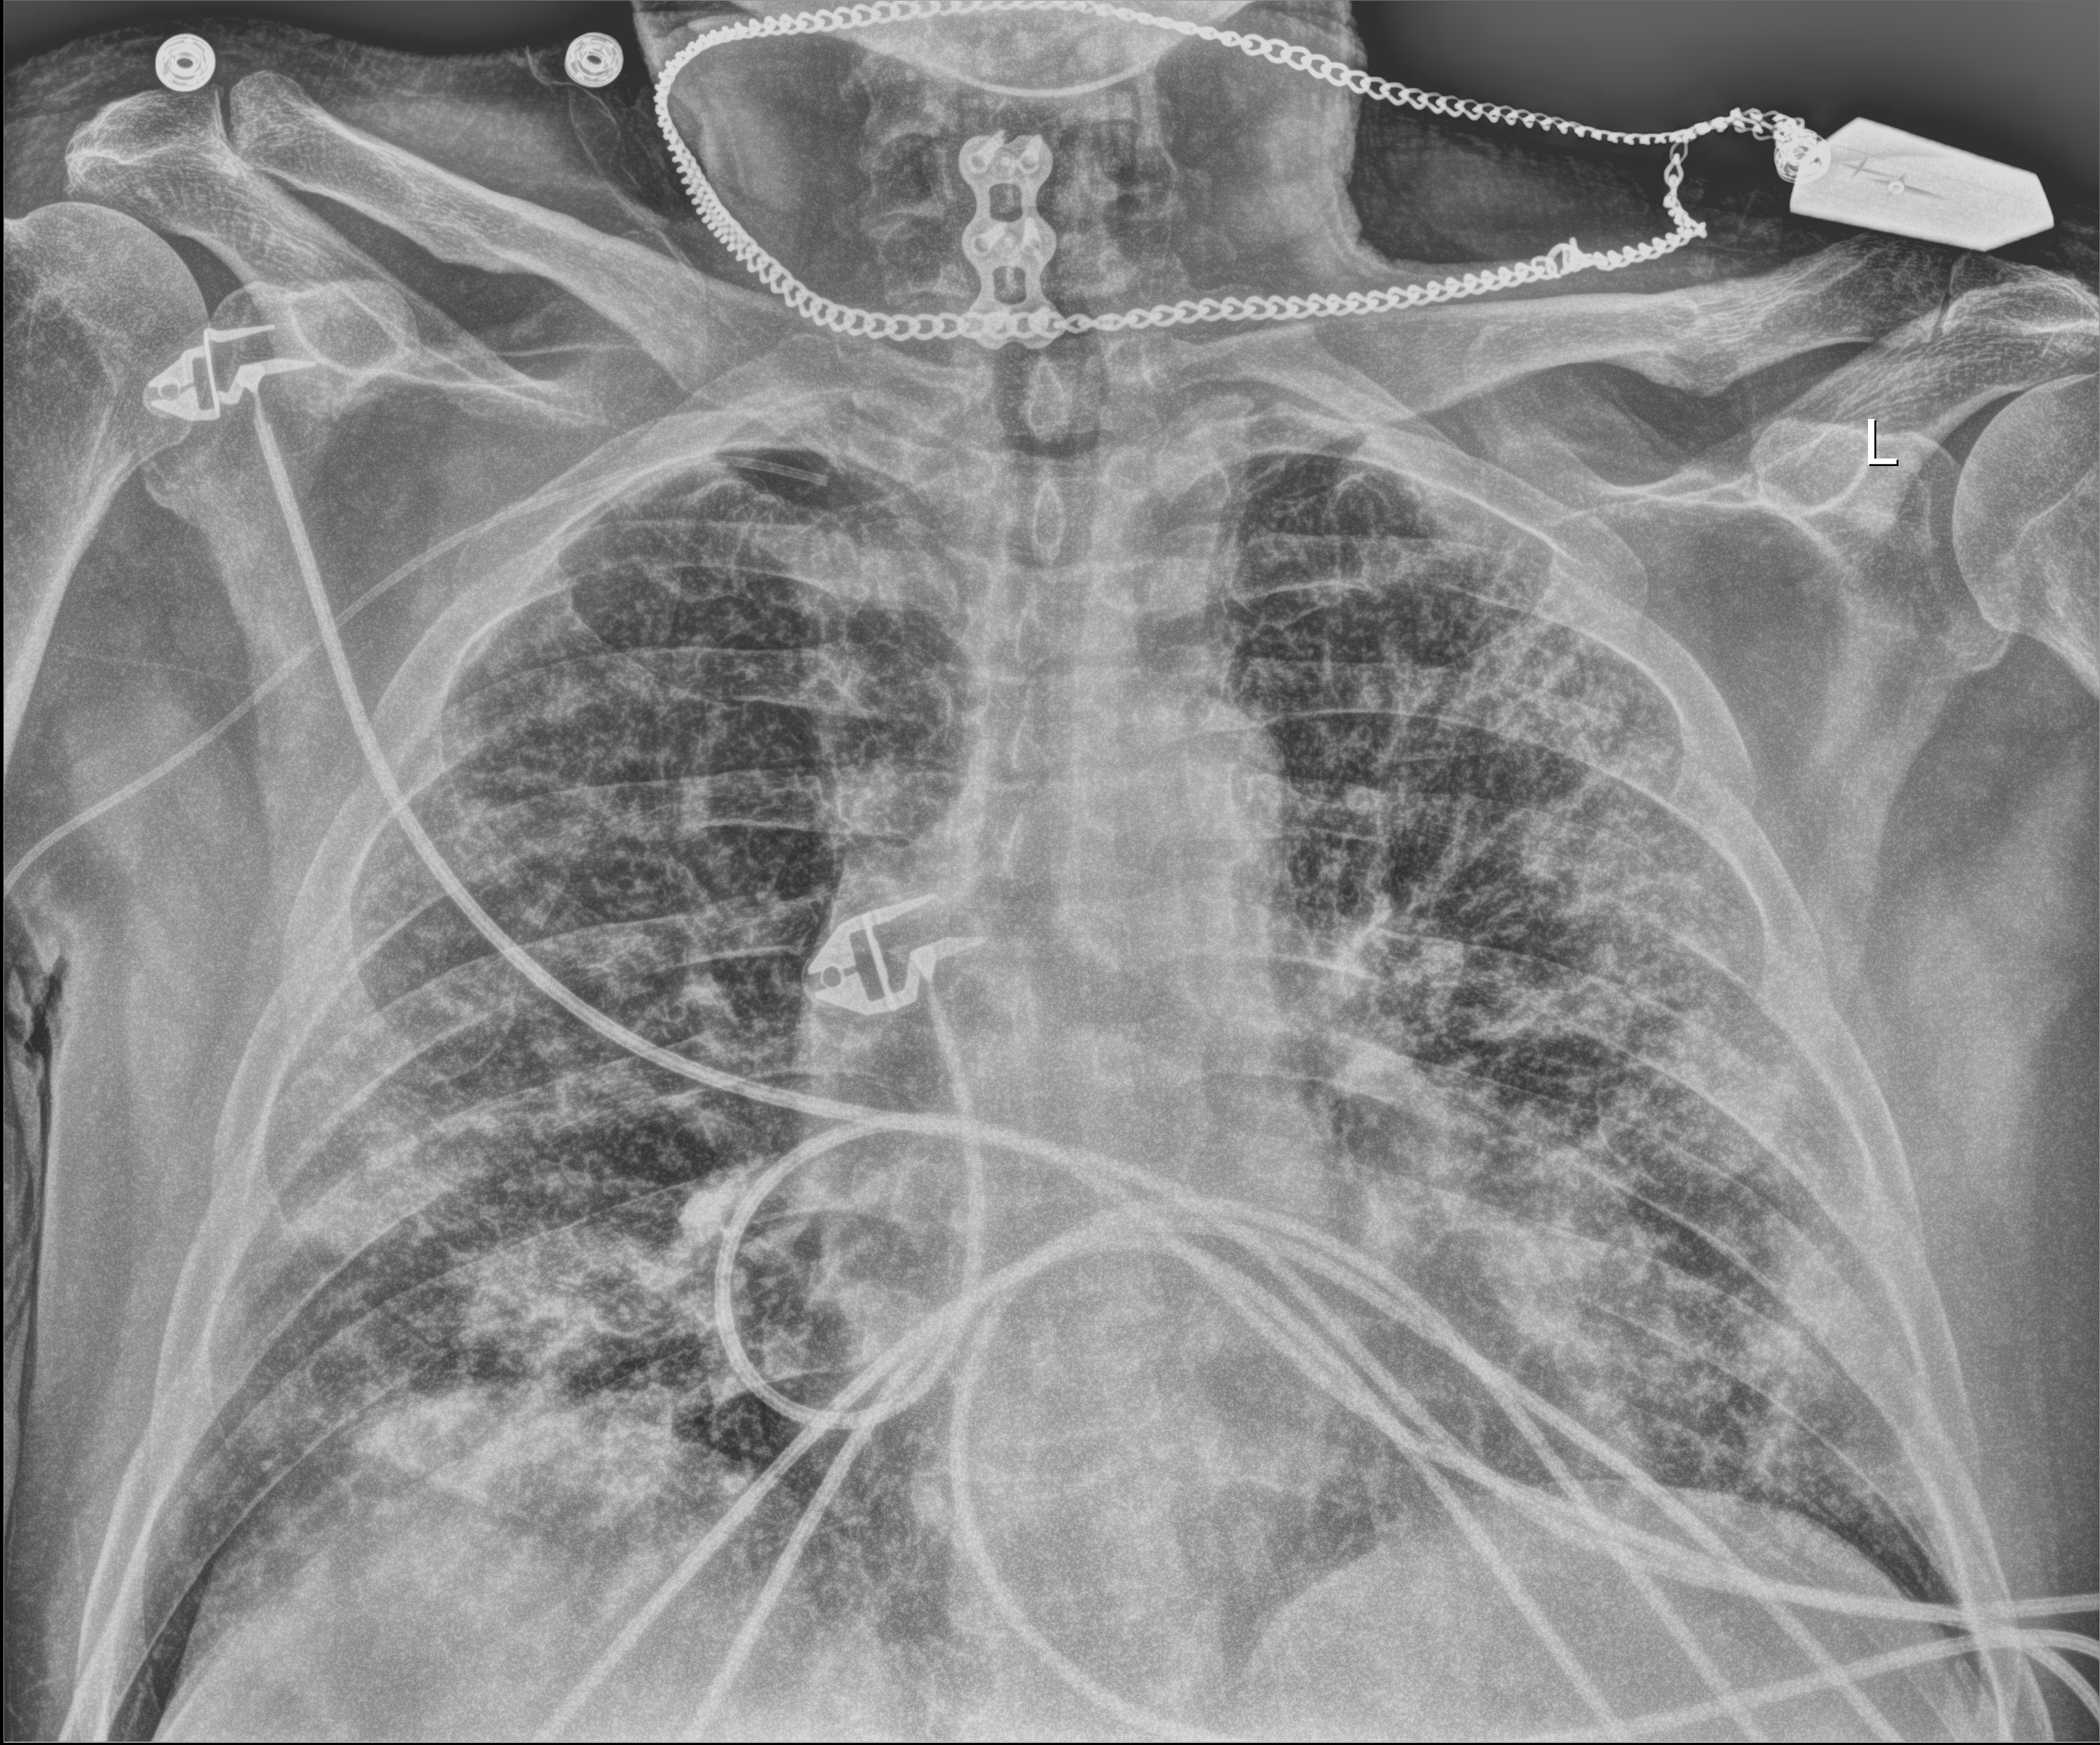
Chest radiograph (digital radiography). Male patient hospitalised with COVID-19, age 60–74 years.
Admission-level facts for this patient (not findings on this image; timing relative to this image not recorded):
- length of hospital stay: 15 days
- admitted to intensive care during this hospital stay: no
- diabetes (admission record): no